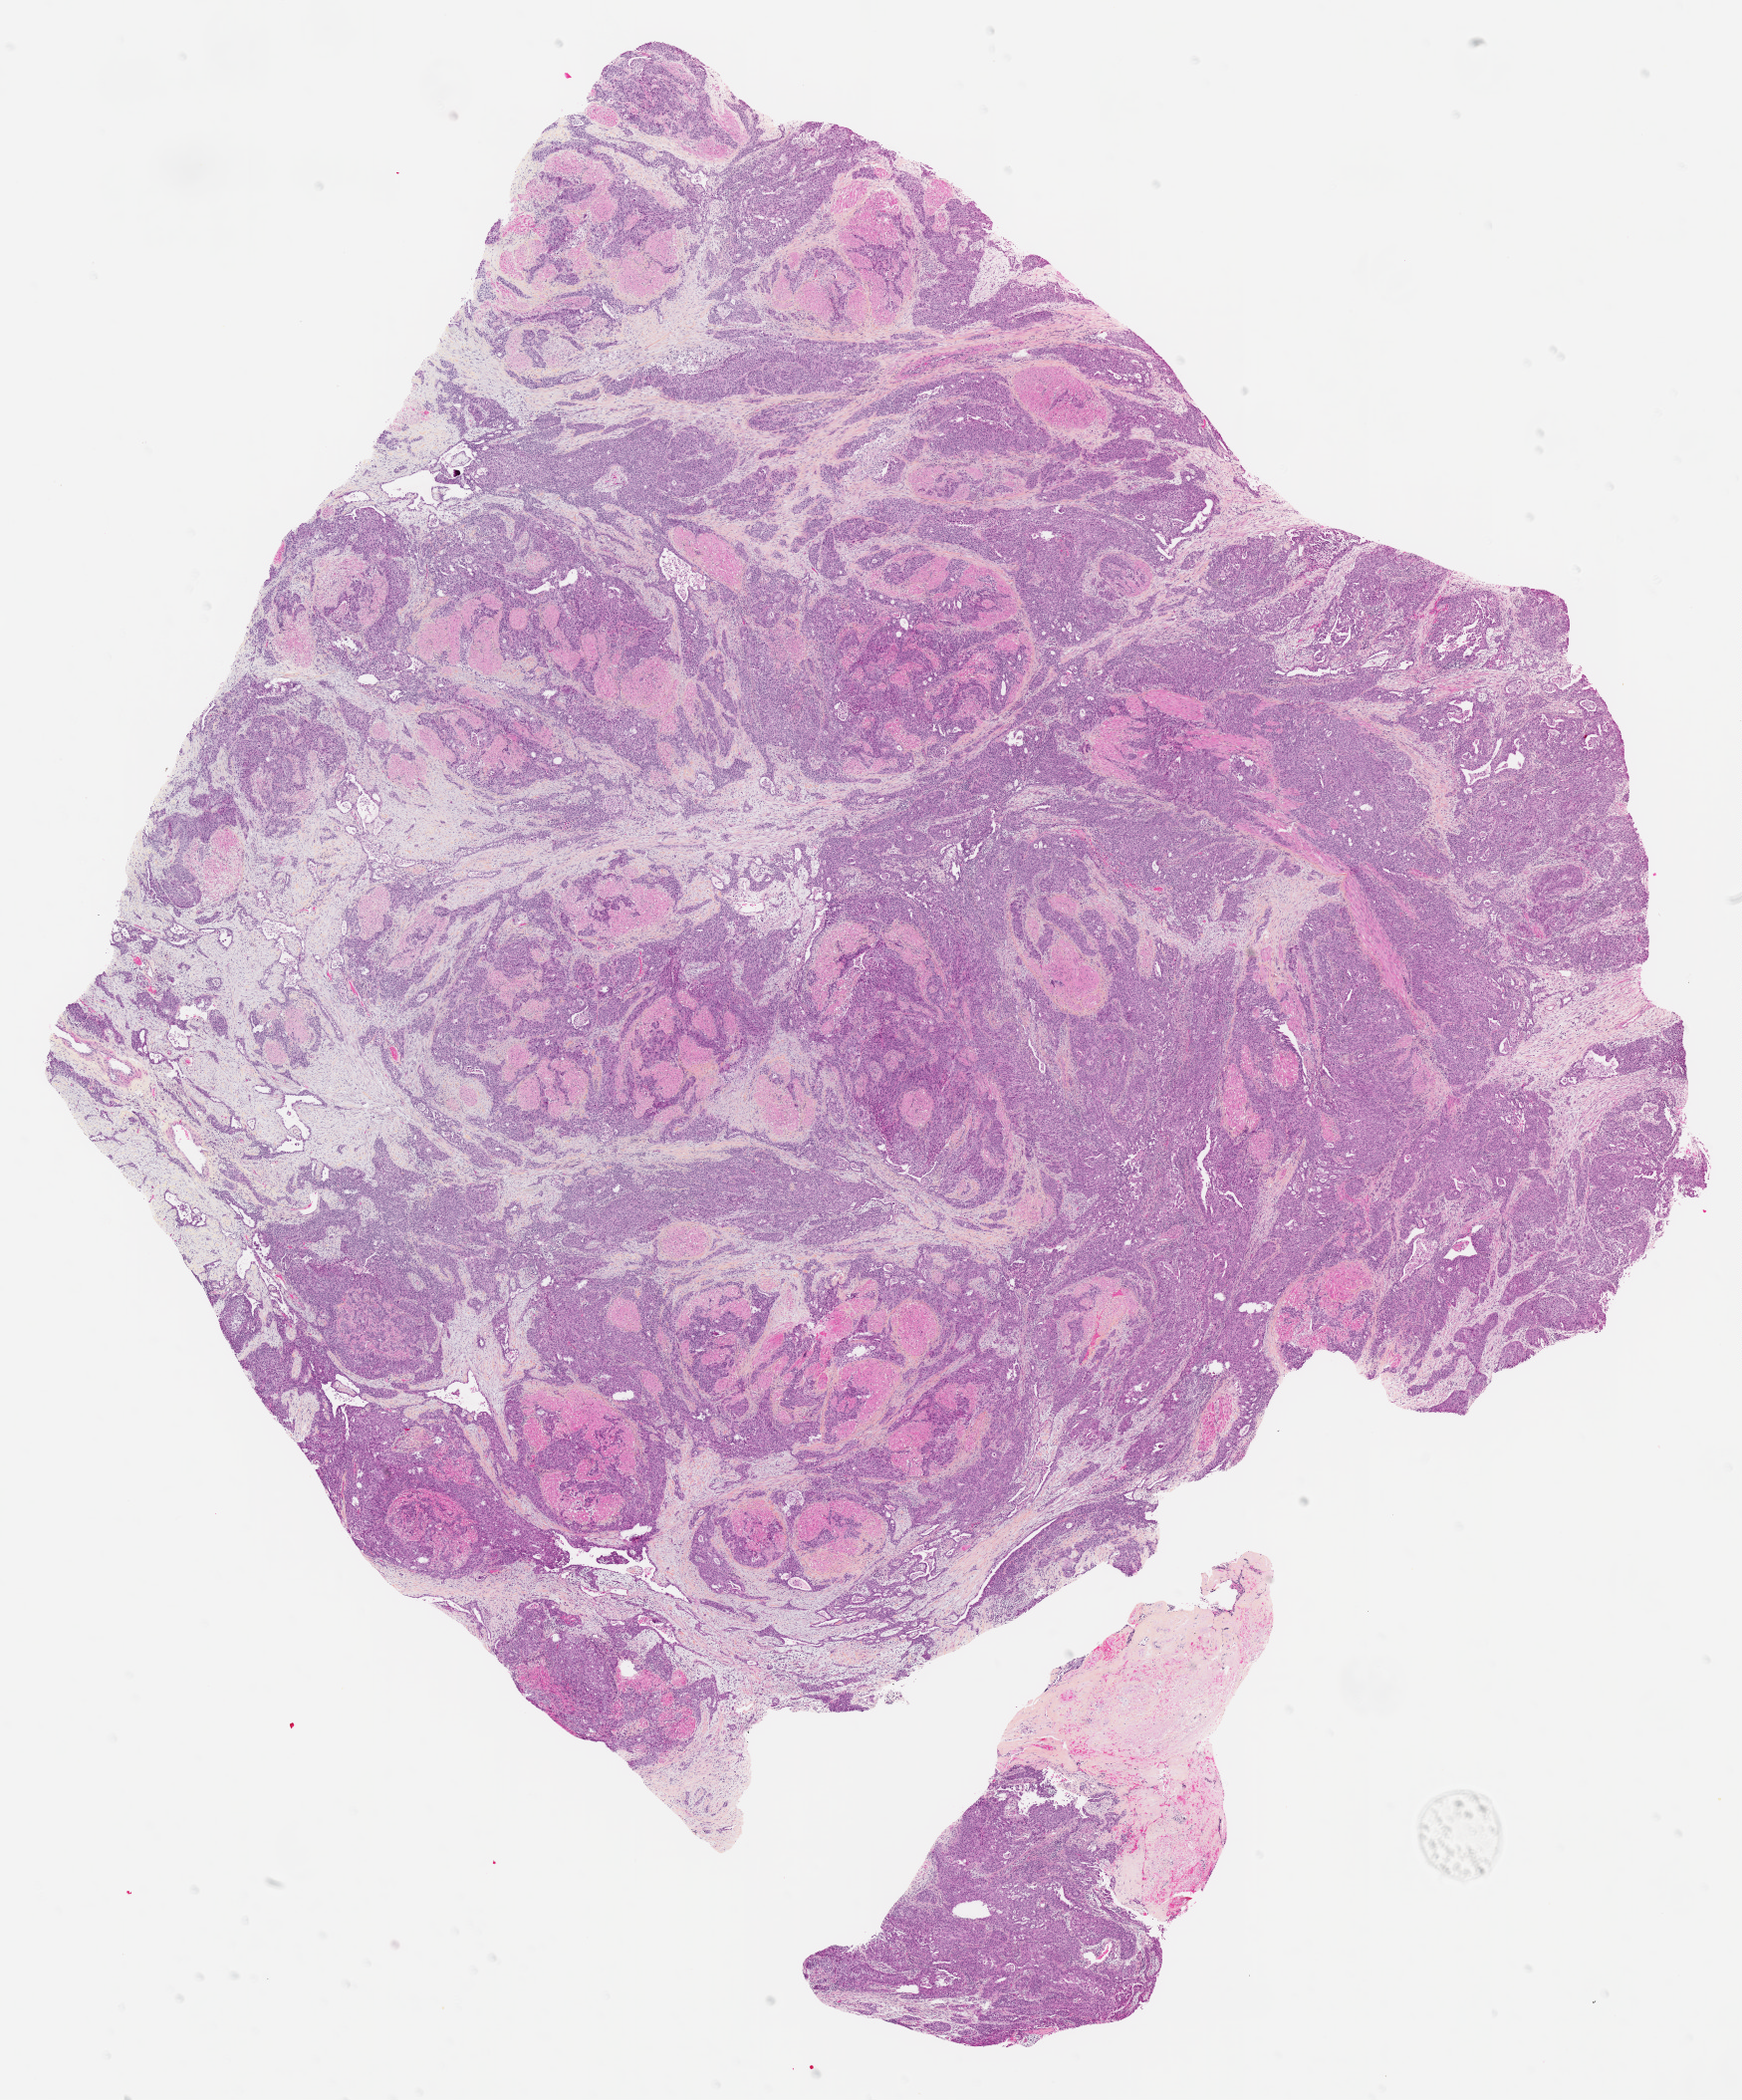
Digitized Hematoxylin and eosin (H&E) stained tissue section (whole slide) — shown as a low-resolution overview of the whole scanned area (about 14.0 x 16.9 mm, from a 20x scan); formalin-fixed paraffin-embedded (FFPE) diagnostic section; primary tumour sample from the bladder. Male, age 78 years at initial diagnosis. Histologic grade: high grade.
AJCC pathologic stage: IV (6th edition). Histologic diagnosis: Transitional cell carcinoma. Lymph nodes positive (case pathology): 1 of 9 examined.